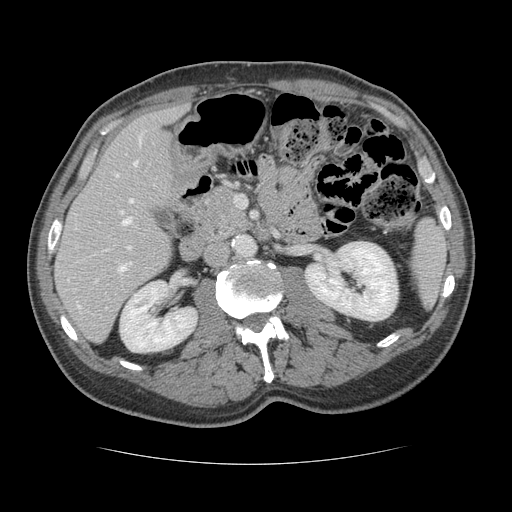
Contrast-enhanced abdominal CT, one axial slice; position 62 of 134 along the scan axis; 120 kVp; intravenous contrast given; soft-tissue window (W 400 / L 40 HU); 2.5 mm slice thickness; 512 × 512 image matrix, field of view 377 × 377 mm. Male patient, age 68 years. From the clinical record (not read from this slice): diagnosis: colorectal cancer liver metastases, imaged before liver resection; multiple liver metastases: yes; largest metastasis: 2.2 cm; disease in both lobes: no.
Annotated regions visible in this slice (expert manual segmentation):
- hepatic veins: bounding box (x1, y1, x2, y2) in pixels: (78, 137, 141, 308)
- liver: (56, 109, 180, 341)
- planned liver remnant (the part of the liver to remain after resection): (56, 109, 180, 335)
- portal vein (with intrahepatic branches): (119, 210, 131, 271)